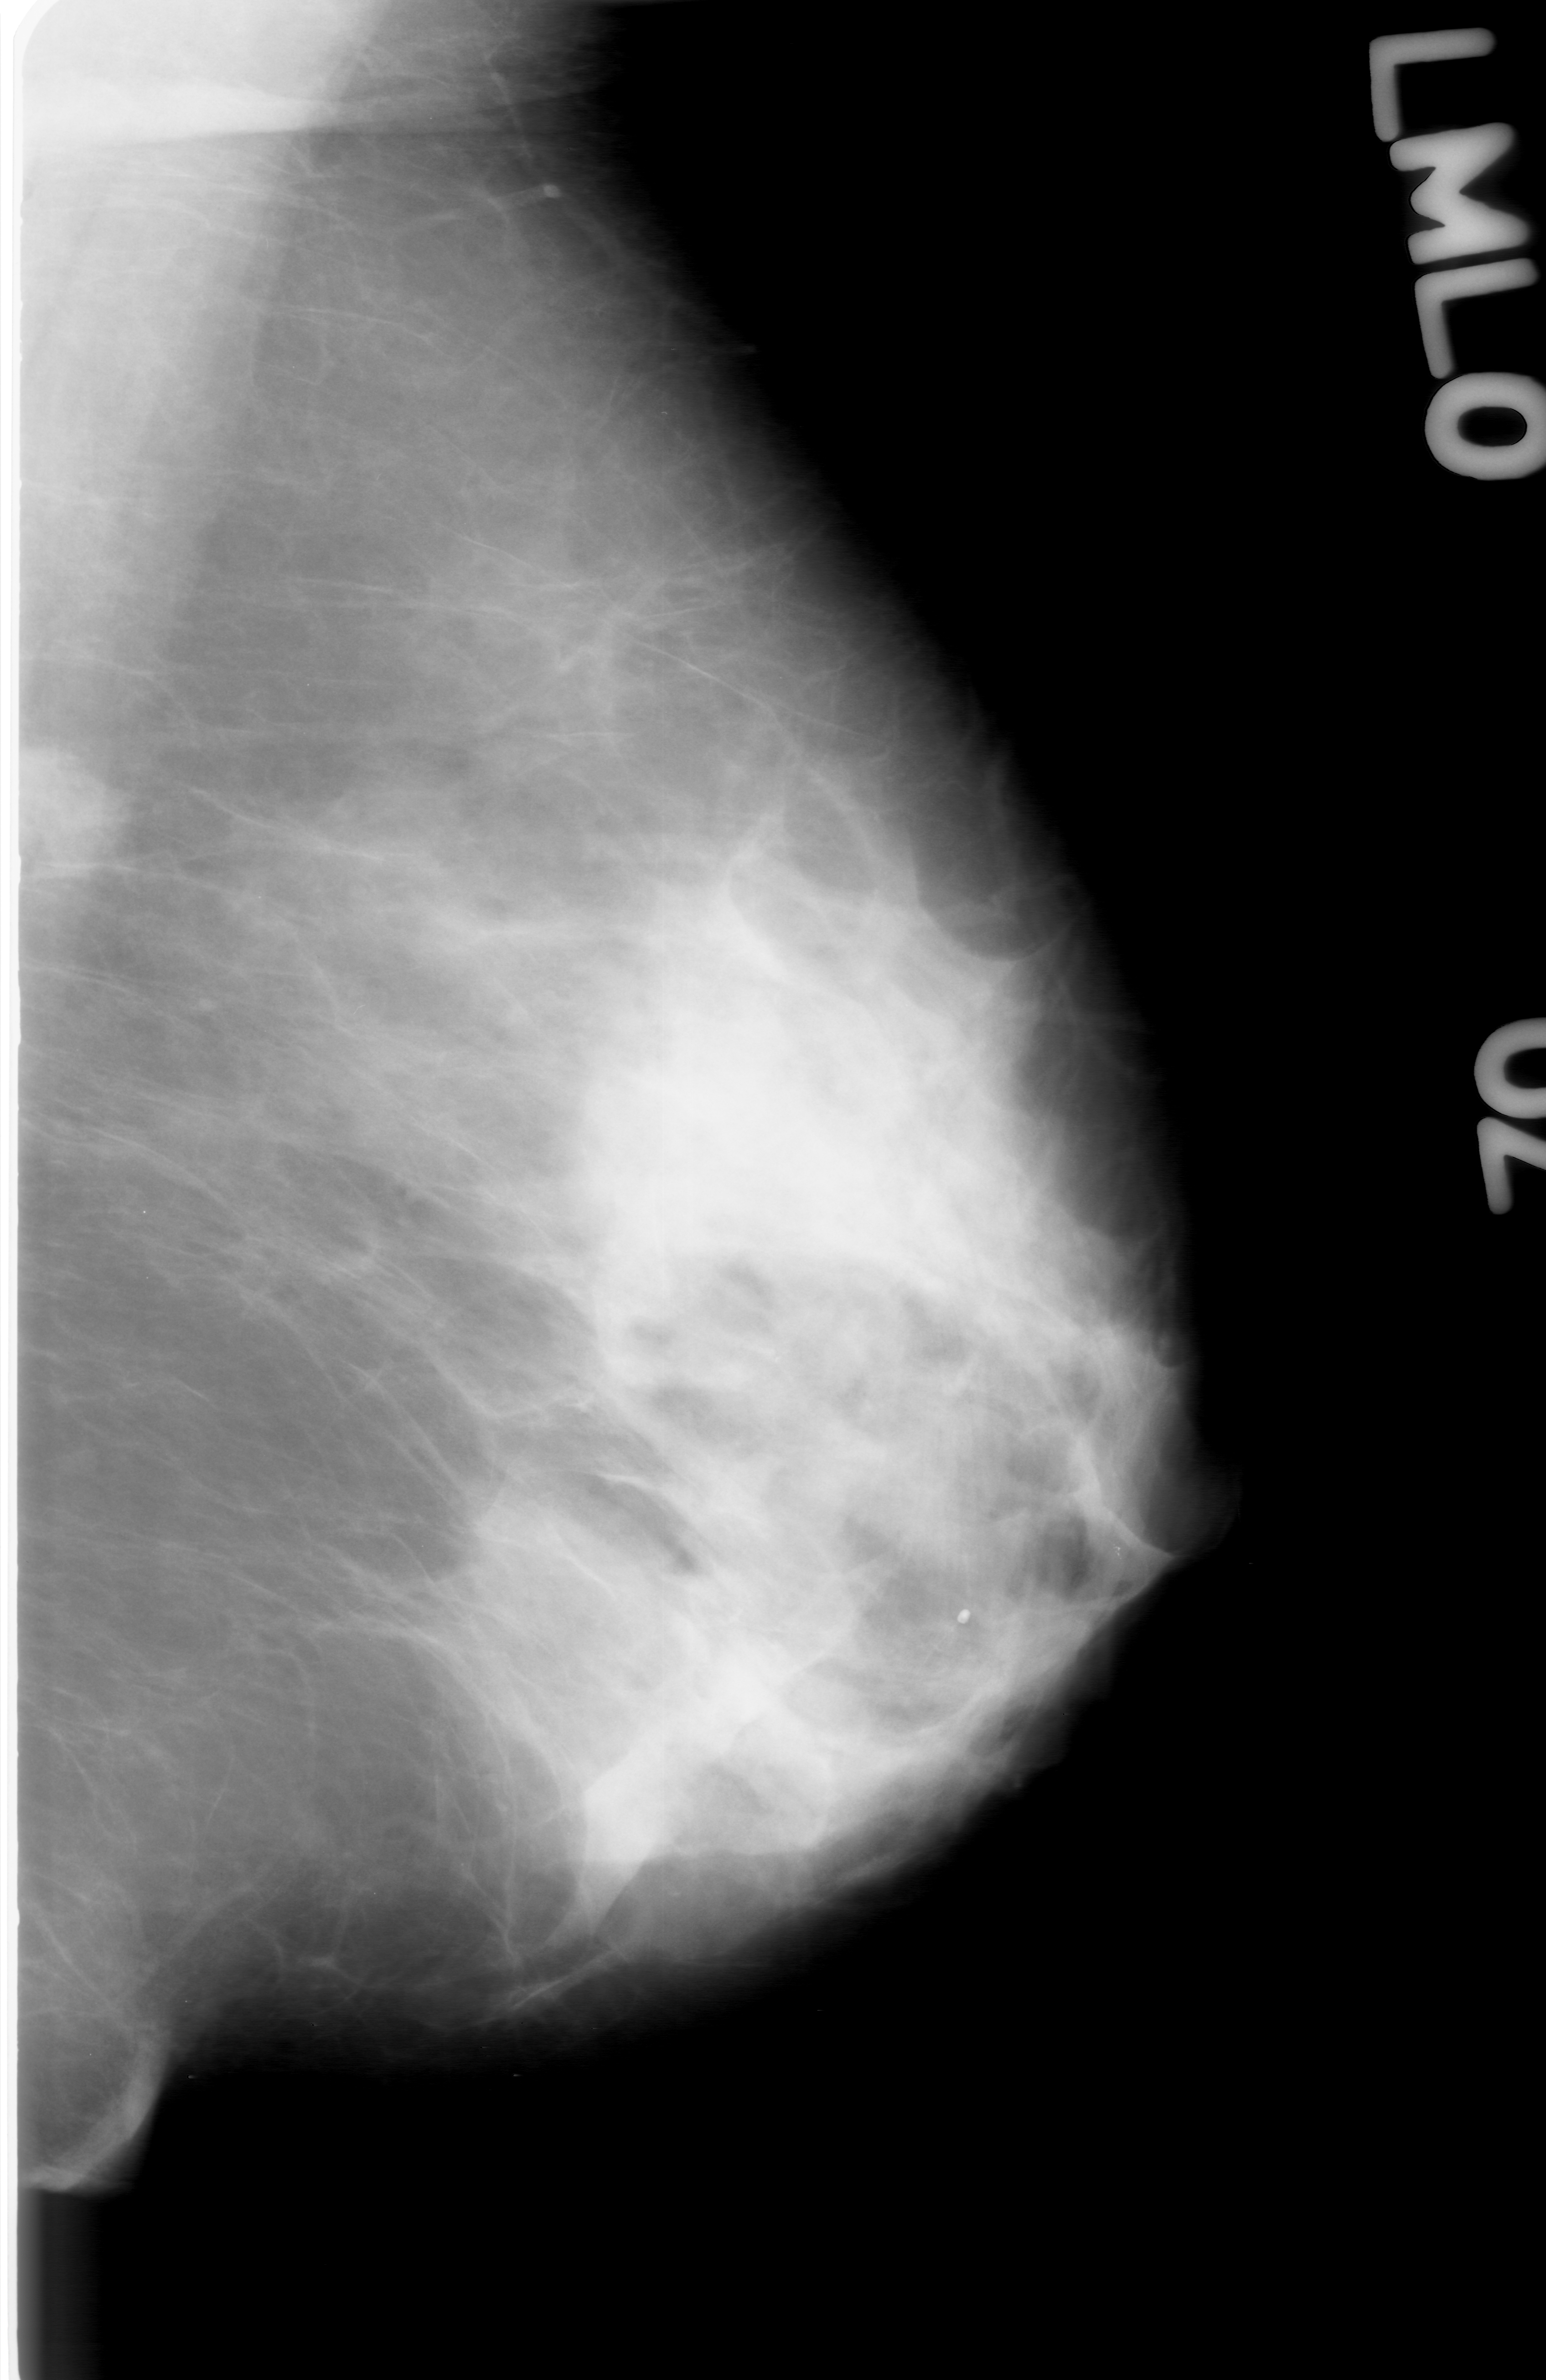
Scanned film-screen mammogram; left breast; mediolateral oblique (MLO) view; breast composition: heterogeneously dense (BI-RADS density category 3 of 4).
Abnormality record for this image: mass, shape irregular, margins ill defined; BI-RADS assessment category 0; subtlety rating 4 on a 1 (subtle) to 5 (obvious) scale; pathology (as recorded): benign.